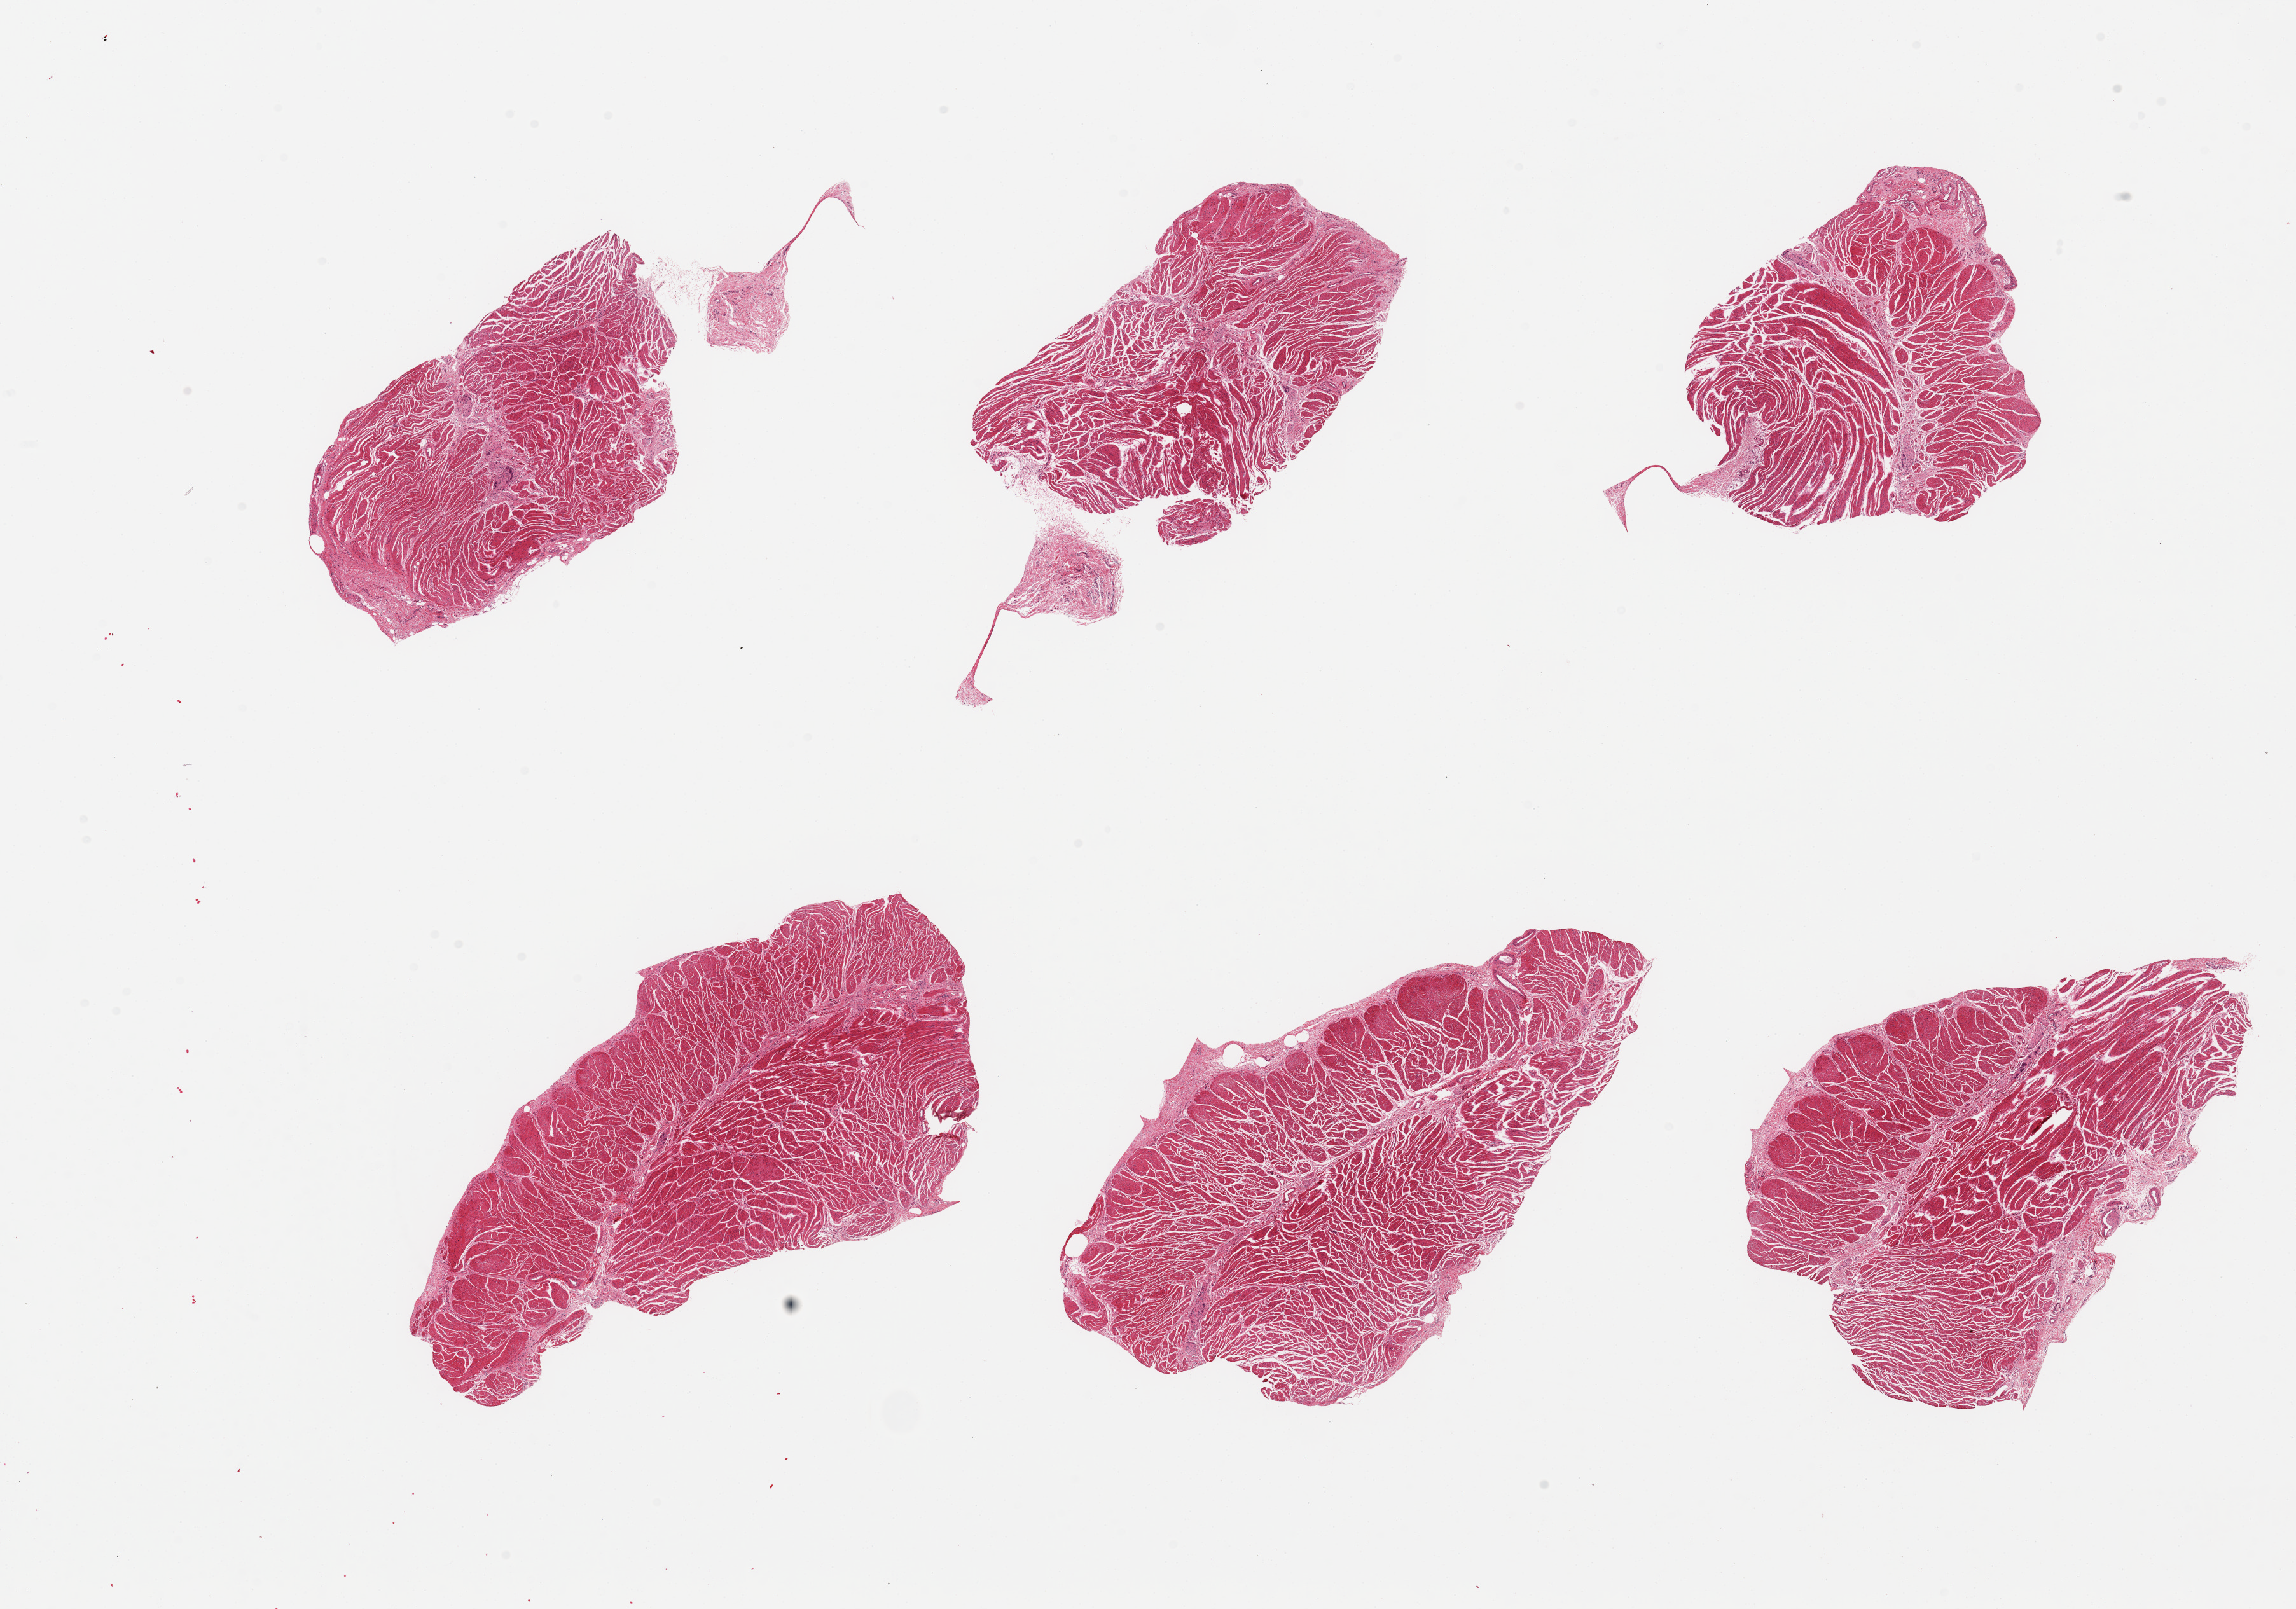
Haematoxylin and eosin whole-slide image, brightfield — whole scanned area (about 28.5 x 20.0 mm) shown as a low-resolution overview; PAXgene-fixed paraffin-embedded (PFPE) section; section of esophageal muscle (target tissue); donor tissue sample. Donor: male.
Reviewer comment on this tissue sample: 6 pieces; well dissected muscularis.